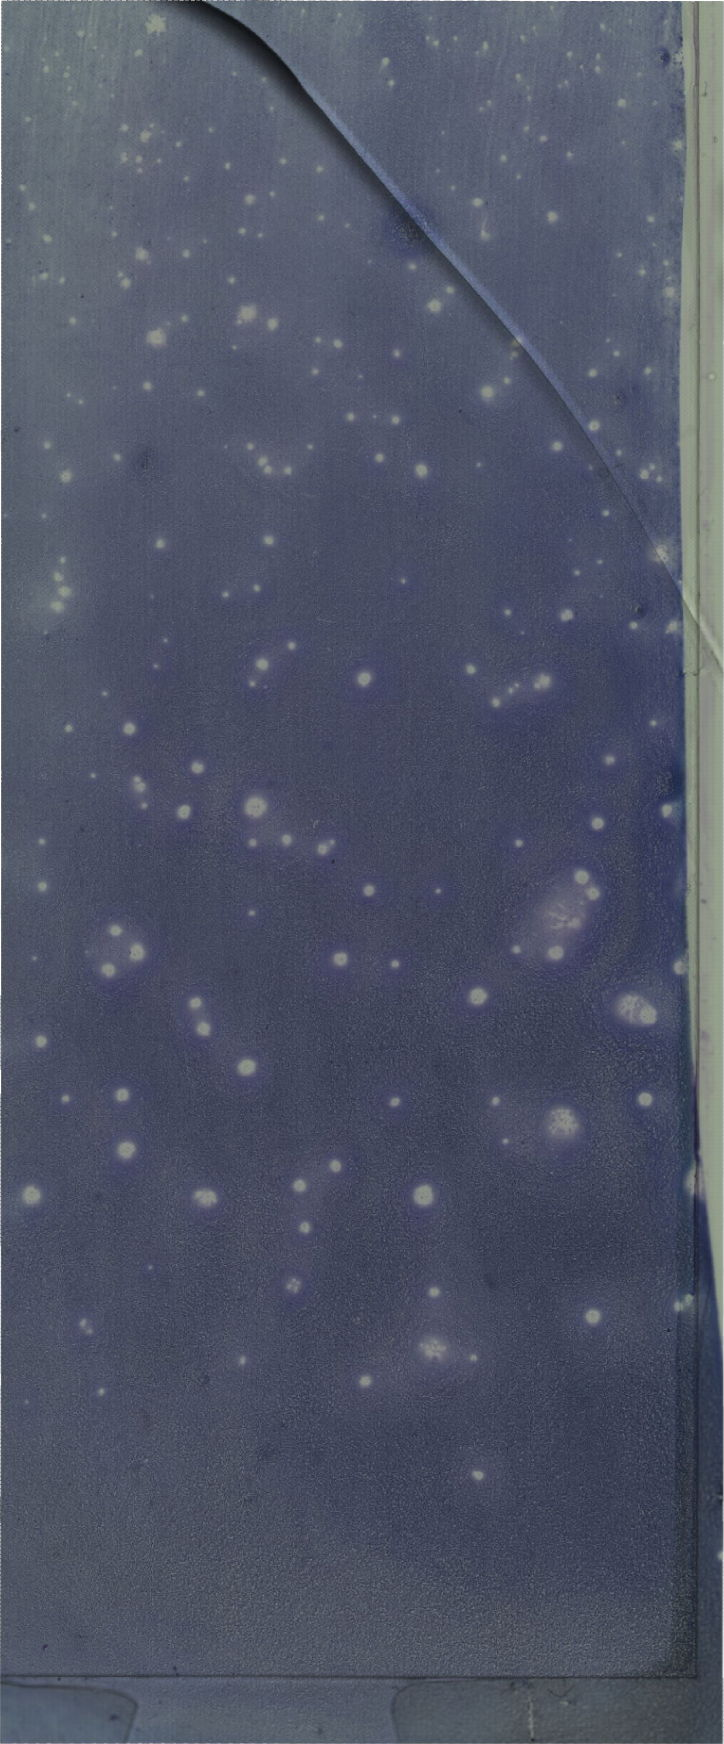
Bone marrow aspirate smear, May-Grünwald–Giemsa stain, whole-slide image, whole scanned area (about 20.5 x 49.4 mm) shown as a low-resolution overview. Female patient.
Diagnosis: Acute Megakaryoblastic Leukemia.